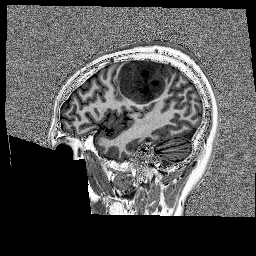
Brain MRI from a brain-tumour surgery series, one sagittal slice. Position 47 of 176 along the scan axis. 256 × 256 image matrix. From the clinical record (not read from this slice): histopathology: Glioblastoma; WHO grade: 4; IDH mutation: no.
Structures marked on this image (outlined manually by an expert reader):
- tumour: bounding box [x1, y1, x2, y2] px = [118, 58, 175, 105]